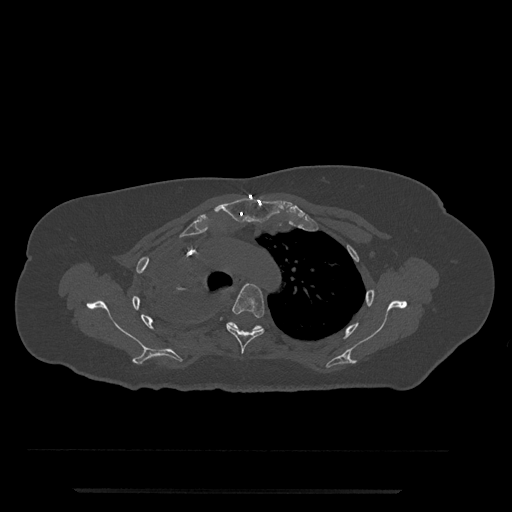
CT including the spine, one axial slice. Position 581 of 797 along the scan axis. Reconstruction kernel Br40s/3. 120 kVp. Bone window (W 1800 / L 400 HU). 0.5 mm slice thickness. 512 × 512 image matrix. Female patient, age 51 years. Case-level facts recorded for this patient, not image findings: primary cancer: neuro; vertebrae with lytic lesions (as recorded): T8.
Annotated regions visible in this slice (semi-automatic segmentation, software-assisted and operator-edited):
- T4 vertebra: box from (x=226, y=283) to (x=265, y=354) px
- T5 vertebra: (x=226, y=322)–(x=264, y=333)